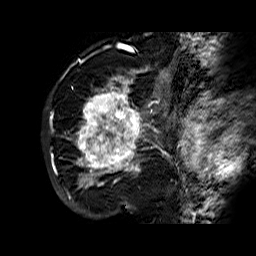
Breast MRI (dynamic contrast-enhanced), one sagittal slice. Position 44 of 60 along the scan axis. Dynamic contrast-enhanced series, time point 2 of 6 at this slice position (early post-contrast). 1.5 T. TE 6.3 ms, TR 32.4 ms. 4 mm slice thickness. 256 × 256 image matrix. Female patient. Case-level facts recorded for this patient, not image findings: setting: breast cancer imaged before/during neoadjuvant chemotherapy; receptor status: HR-positive, HER2-negative.
Structures marked on this image (semi-automatically segmented with operator editing):
- analysis volume of interest (the breast-tissue region the enhancement analysis was run in; not a lesion): bounding box <68,72,177,183> (left, top, right, bottom; pixels)
- tumour enhancement mask (voxels above the 100 % enhancement threshold inside the analysis volume of interest): <75,72,168,183>